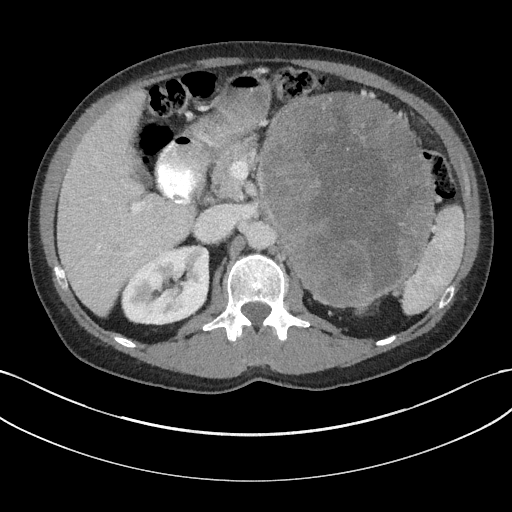
Contrast-enhanced abdominal CT, one axial slice. Position 108 of 147 along the scan axis. Reconstruction kernel I31f/3. 100 kVp. Intravenous contrast given. Soft-tissue window (W 400 / L 40 HU). 512 × 512 image matrix, field of view 384 × 384 mm. Patient: male, 58 years. Case-level facts recorded for this patient, not image findings: diagnosis: adrenocortical carcinoma; tumour side: left adrenal; tumour size at pathology: 22 cm; Ki-67 index: 26 %; stage (as recorded): 2.
Structures marked on this image (semi-automatically segmented with operator editing):
- mass: bounding box (x1, y1, x2, y2) in pixels: (261, 95, 435, 306)